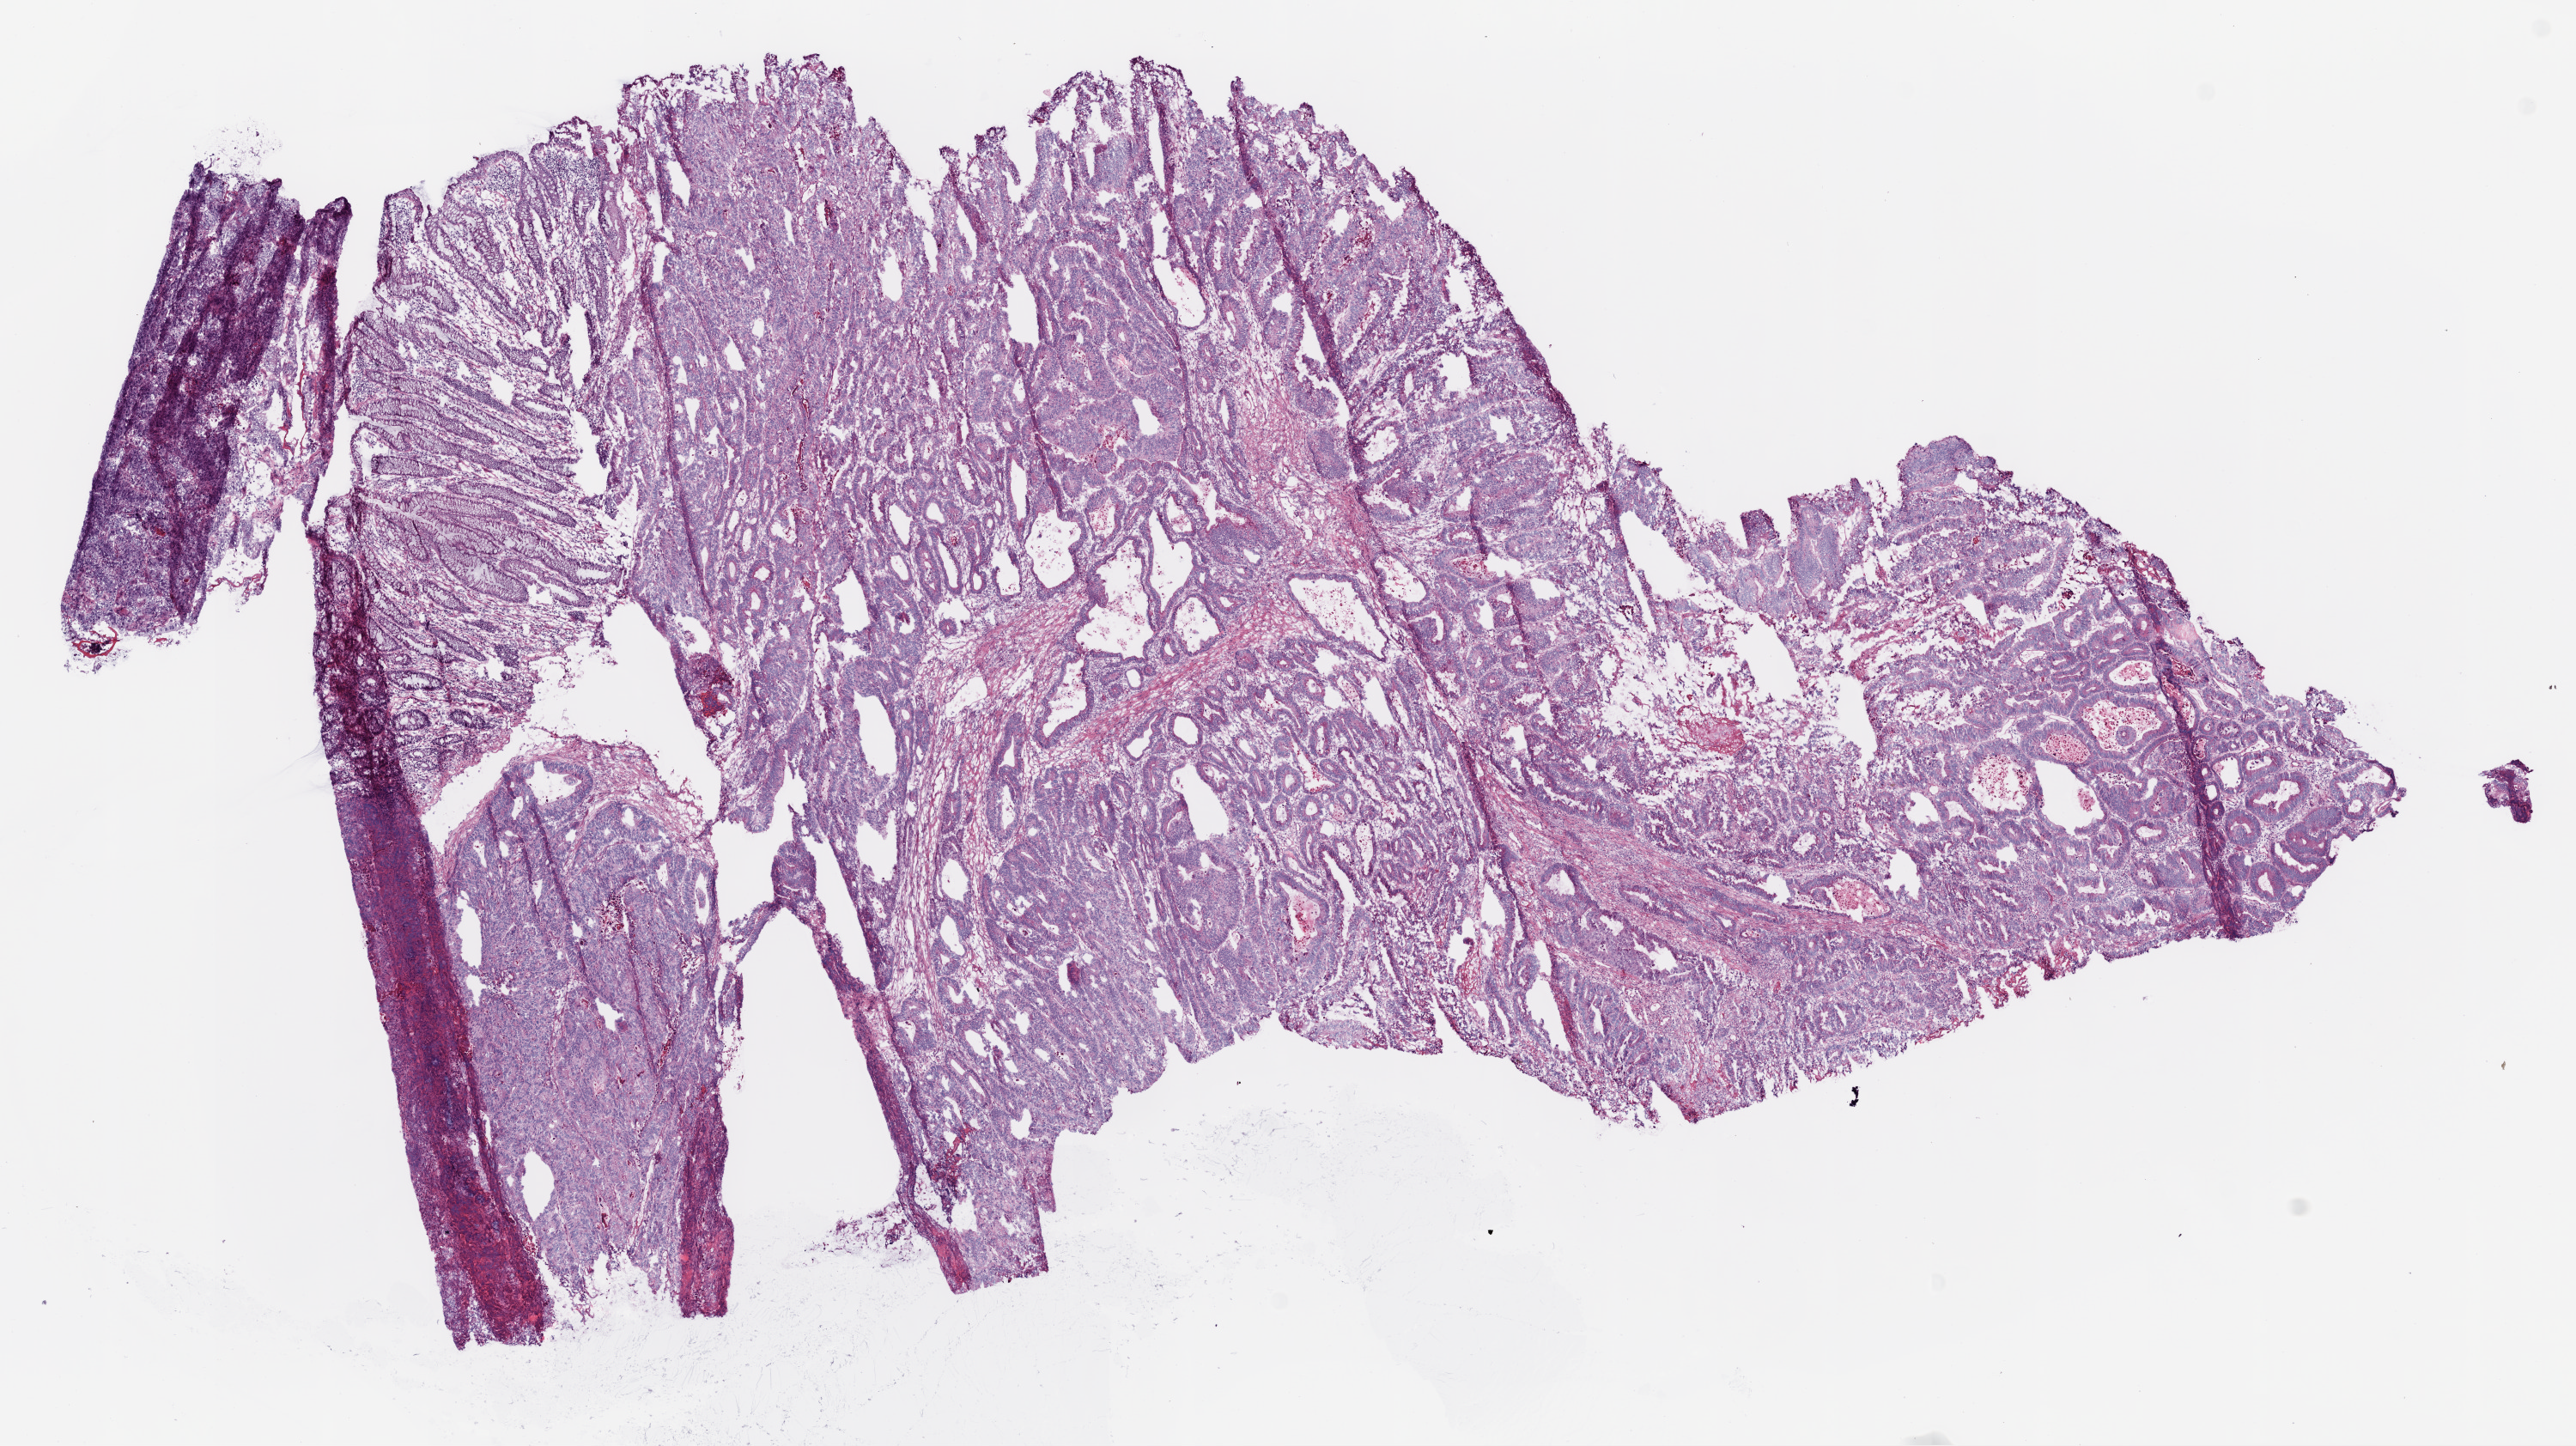
H&E-stained whole-slide image, whole scanned area (about 12.0 x 6.8 mm, from a 20x scan) shown as a low-resolution overview, frozen section from the top of the tissue portion, primary tumour sample from the colon. Patient: male, age at initial diagnosis 77 years.
Pathologic diagnosis: Adenocarcinoma, NOS.